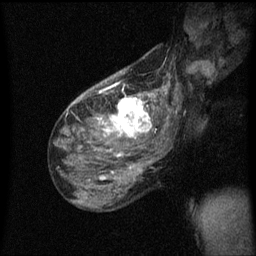
Breast MRI (dynamic contrast-enhanced), one sagittal slice. Position 35 of 60 along the scan axis. Dynamic contrast-enhanced series, image 2 of 3 at this slice position (ordered by acquisition). 1.5 T. TE 4.2 ms, TR 8.4 ms. 2 mm slice thickness. 256 × 256 image matrix, field of view 200 × 200 mm. Patient: female, 49 years.
Structures marked on this image (semi-automatically segmented with operator editing):
- analysis volume of interest (the breast-tissue region the enhancement analysis was run in; not a lesion): box from (x=103, y=90) to (x=157, y=151) px
- tumour enhancement mask (voxels above the 70 % enhancement threshold inside the analysis volume of interest): (x=103, y=90)–(x=156, y=139)